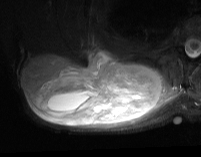
MRI of an extremity soft-tissue mass, one axial slice; position 34 of 74 along the scan axis; STIR; MR volume resampled by the dataset authors to the PET/CT grid (not the native acquisition matrix); 201 × 157 image matrix. Male patient. Case-level facts recorded for this patient, not image findings: histological type: pleiomorphic spindle cell undifferentiated; grade: high; site of the primary tumour: right parascapusular.
Annotated regions visible in this slice (expert contour drawn on MRI and transferred to this co-registered scan by the dataset authors):
- gross tumour volume including surrounding oedema: box from (x=23, y=50) to (x=180, y=129) px
- gross tumour volume (mass): (x=23, y=50)–(x=164, y=126)